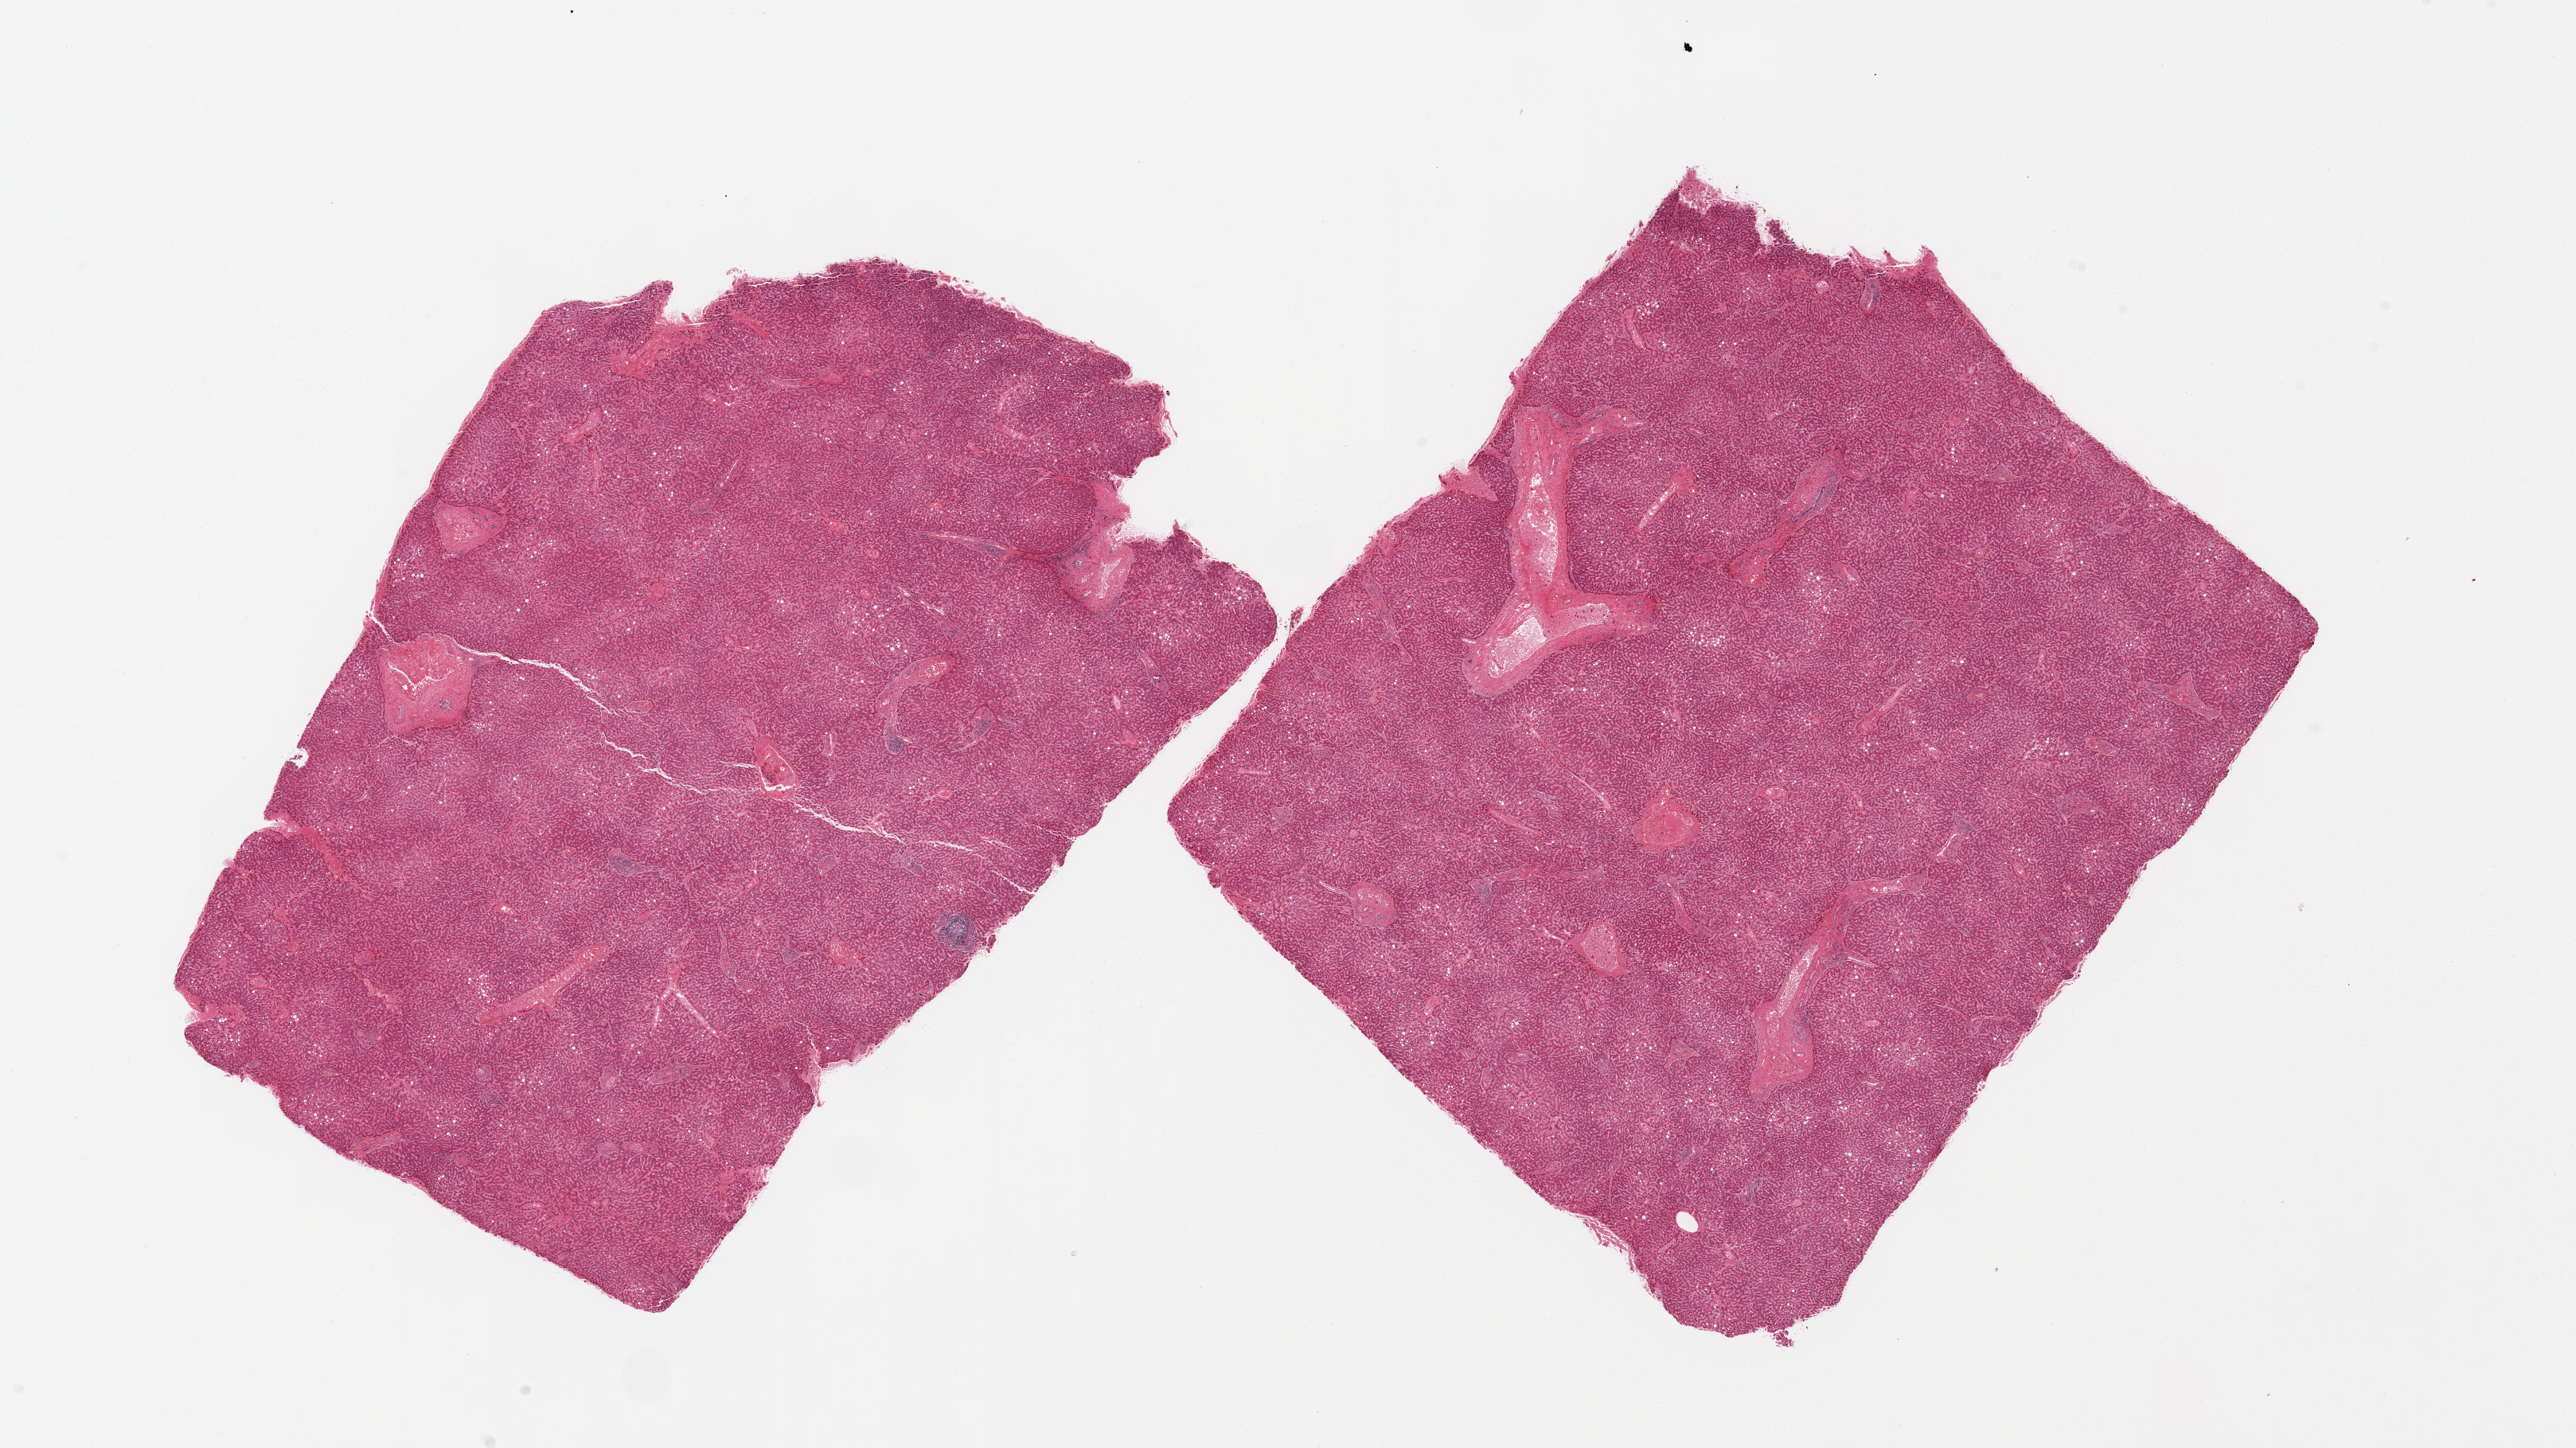
H&E whole-slide image, low-resolution overview of the scanned area, about 25.6 x 14.4 mm (acquisition: 20x scan). PAXgene-fixed, paraffin-embedded tissue. Sampled site (target tissue): liver. Donor tissue sample.
Reviewer comment on this tissue sample: 2 pieces, mild macrovesicular steatosis; moderate passive congestion.